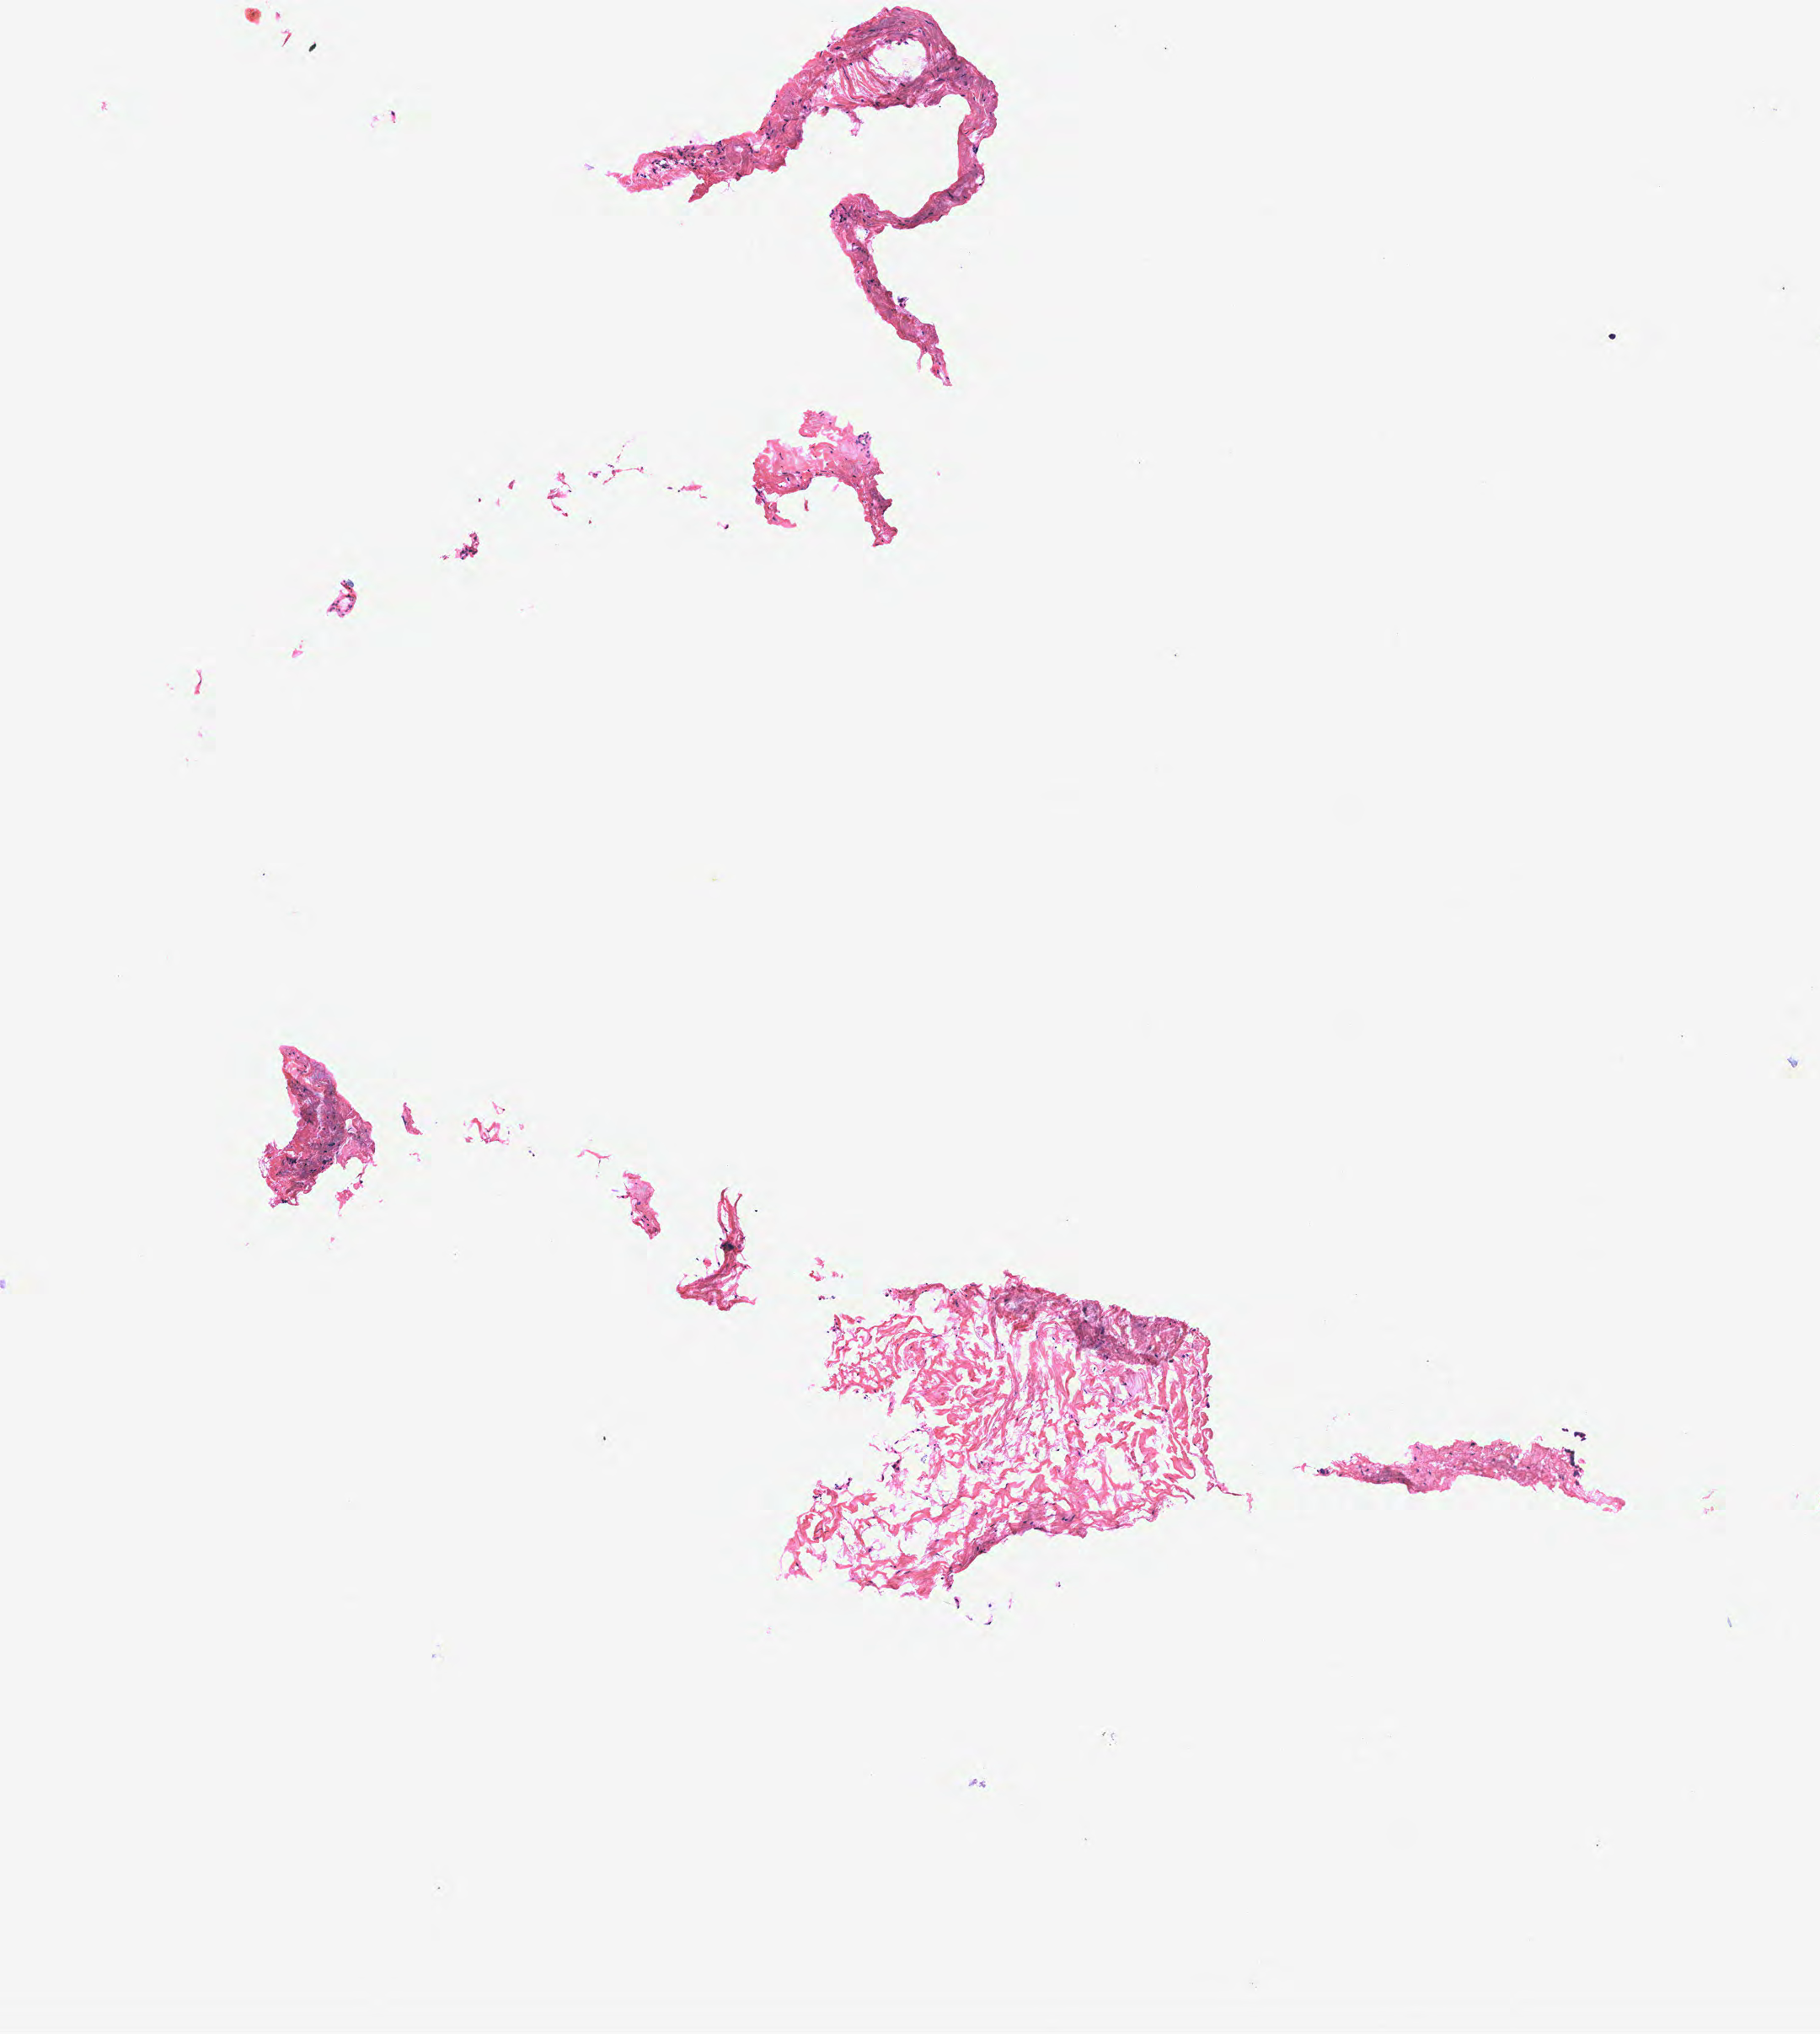
H&E-stained whole-slide image, shown as a low-resolution overview of the whole scanned area (about 4.3 x 4.8 mm), breast, tumour tissue. 72-year-old female patient.
Histologic diagnosis: Infiltrating duct carcinoma, NOS.